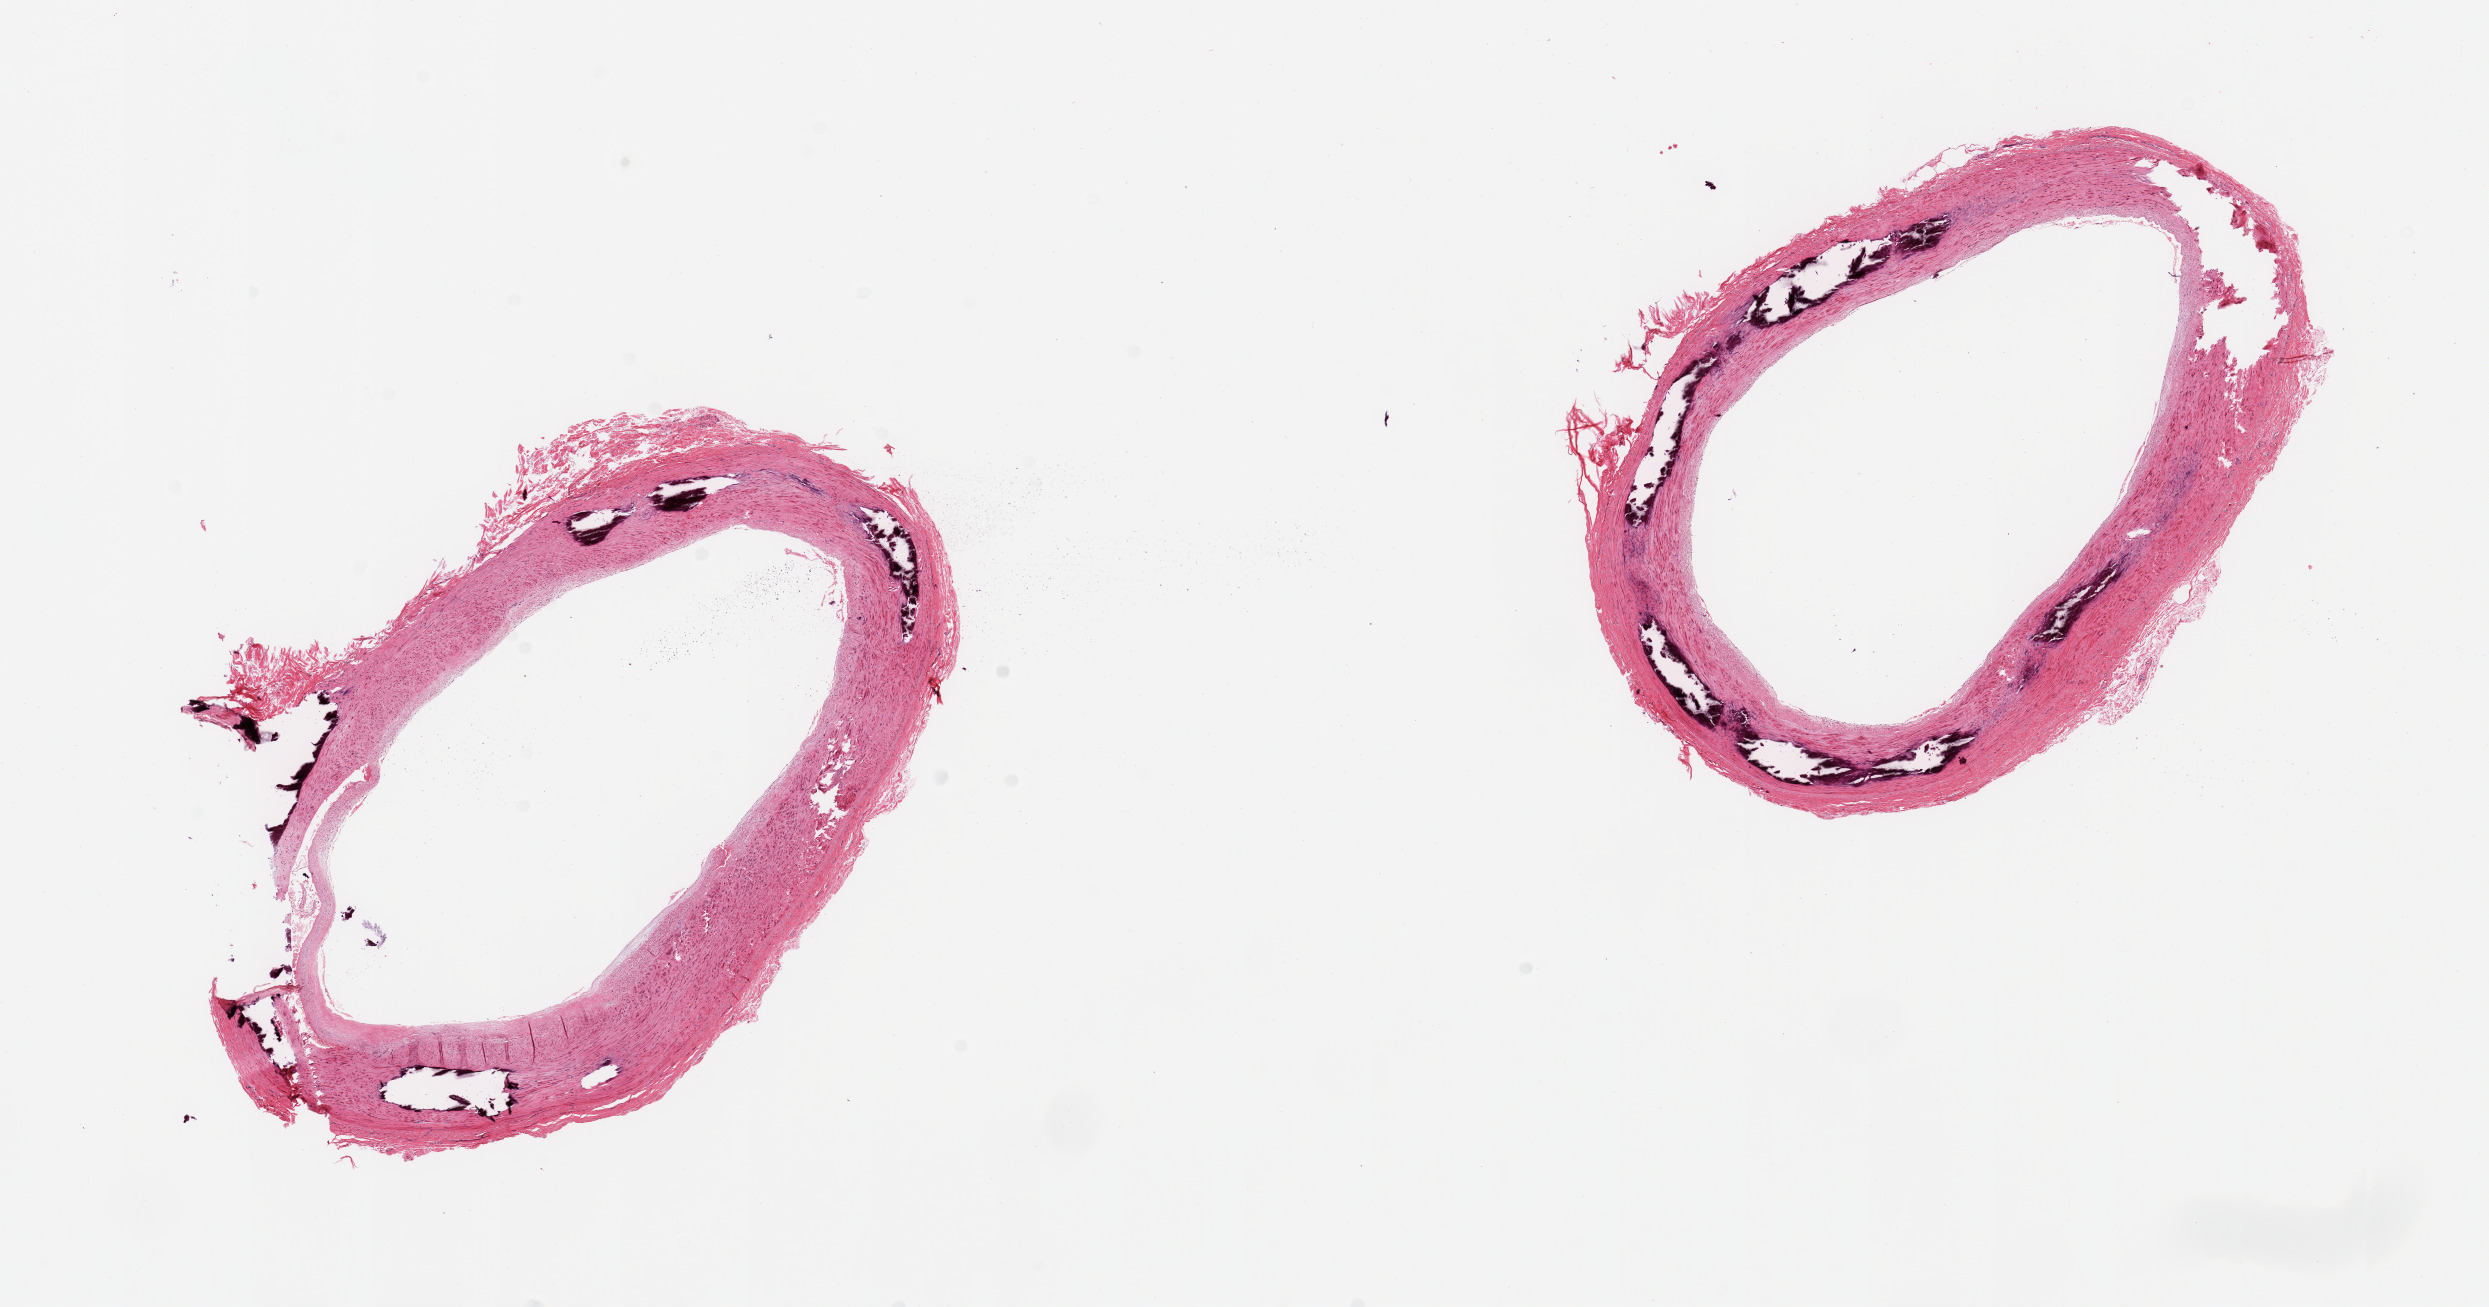
Digitized H&E-stained section — shown as a low-resolution overview of the whole scanned area (about 19.7 x 10.3 mm); PAXgene-fixed paraffin-embedded (PFPE) section; target tissue: tibial artery; tissue donor sample. Donor sex: male.
Pathologist's review note for this sample: 2 pieces, prominent Monckeberg sclerosis; minimal atherosis; not adherent fat.